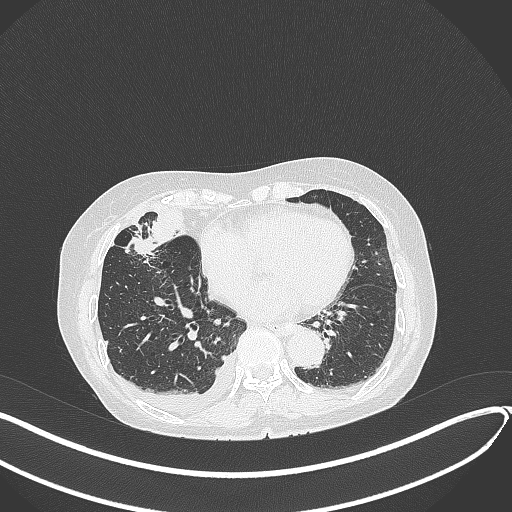
Chest CT, one axial slice; position 142 of 418 along the scan axis; 120 kVp; lung window (W 1500 / L -600 HU); 1 mm slice thickness; 512 × 512 image matrix, field of view 400 × 400 mm. Patient: female, 75 years. From the clinical record (not read from this slice): clinical TNM (as recorded): T2a N3 M0.
Annotated regions visible in this slice (rectangle marked by the reading radiologist):
- lung tumour (recorded histology: adenocarcinoma): bounding box <125,230,159,257> (left, top, right, bottom; pixels)